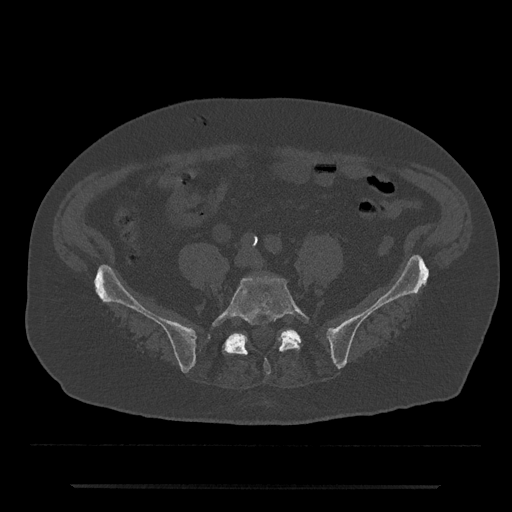
CT including the spine, one axial slice; position 279 of 797 along the scan axis; reconstruction kernel Br40s/3; 120 kVp; bone window (W 1800 / L 400 HU); 512 × 512 image matrix, field of view 434 × 434 mm. Patient: male, 80 years. From the clinical record (not read from this slice): primary cancer: prostate.
Annotated regions visible in this slice (semi-automatically segmented with operator editing):
- L5 vertebra: box from (x=212, y=277) to (x=309, y=374) px